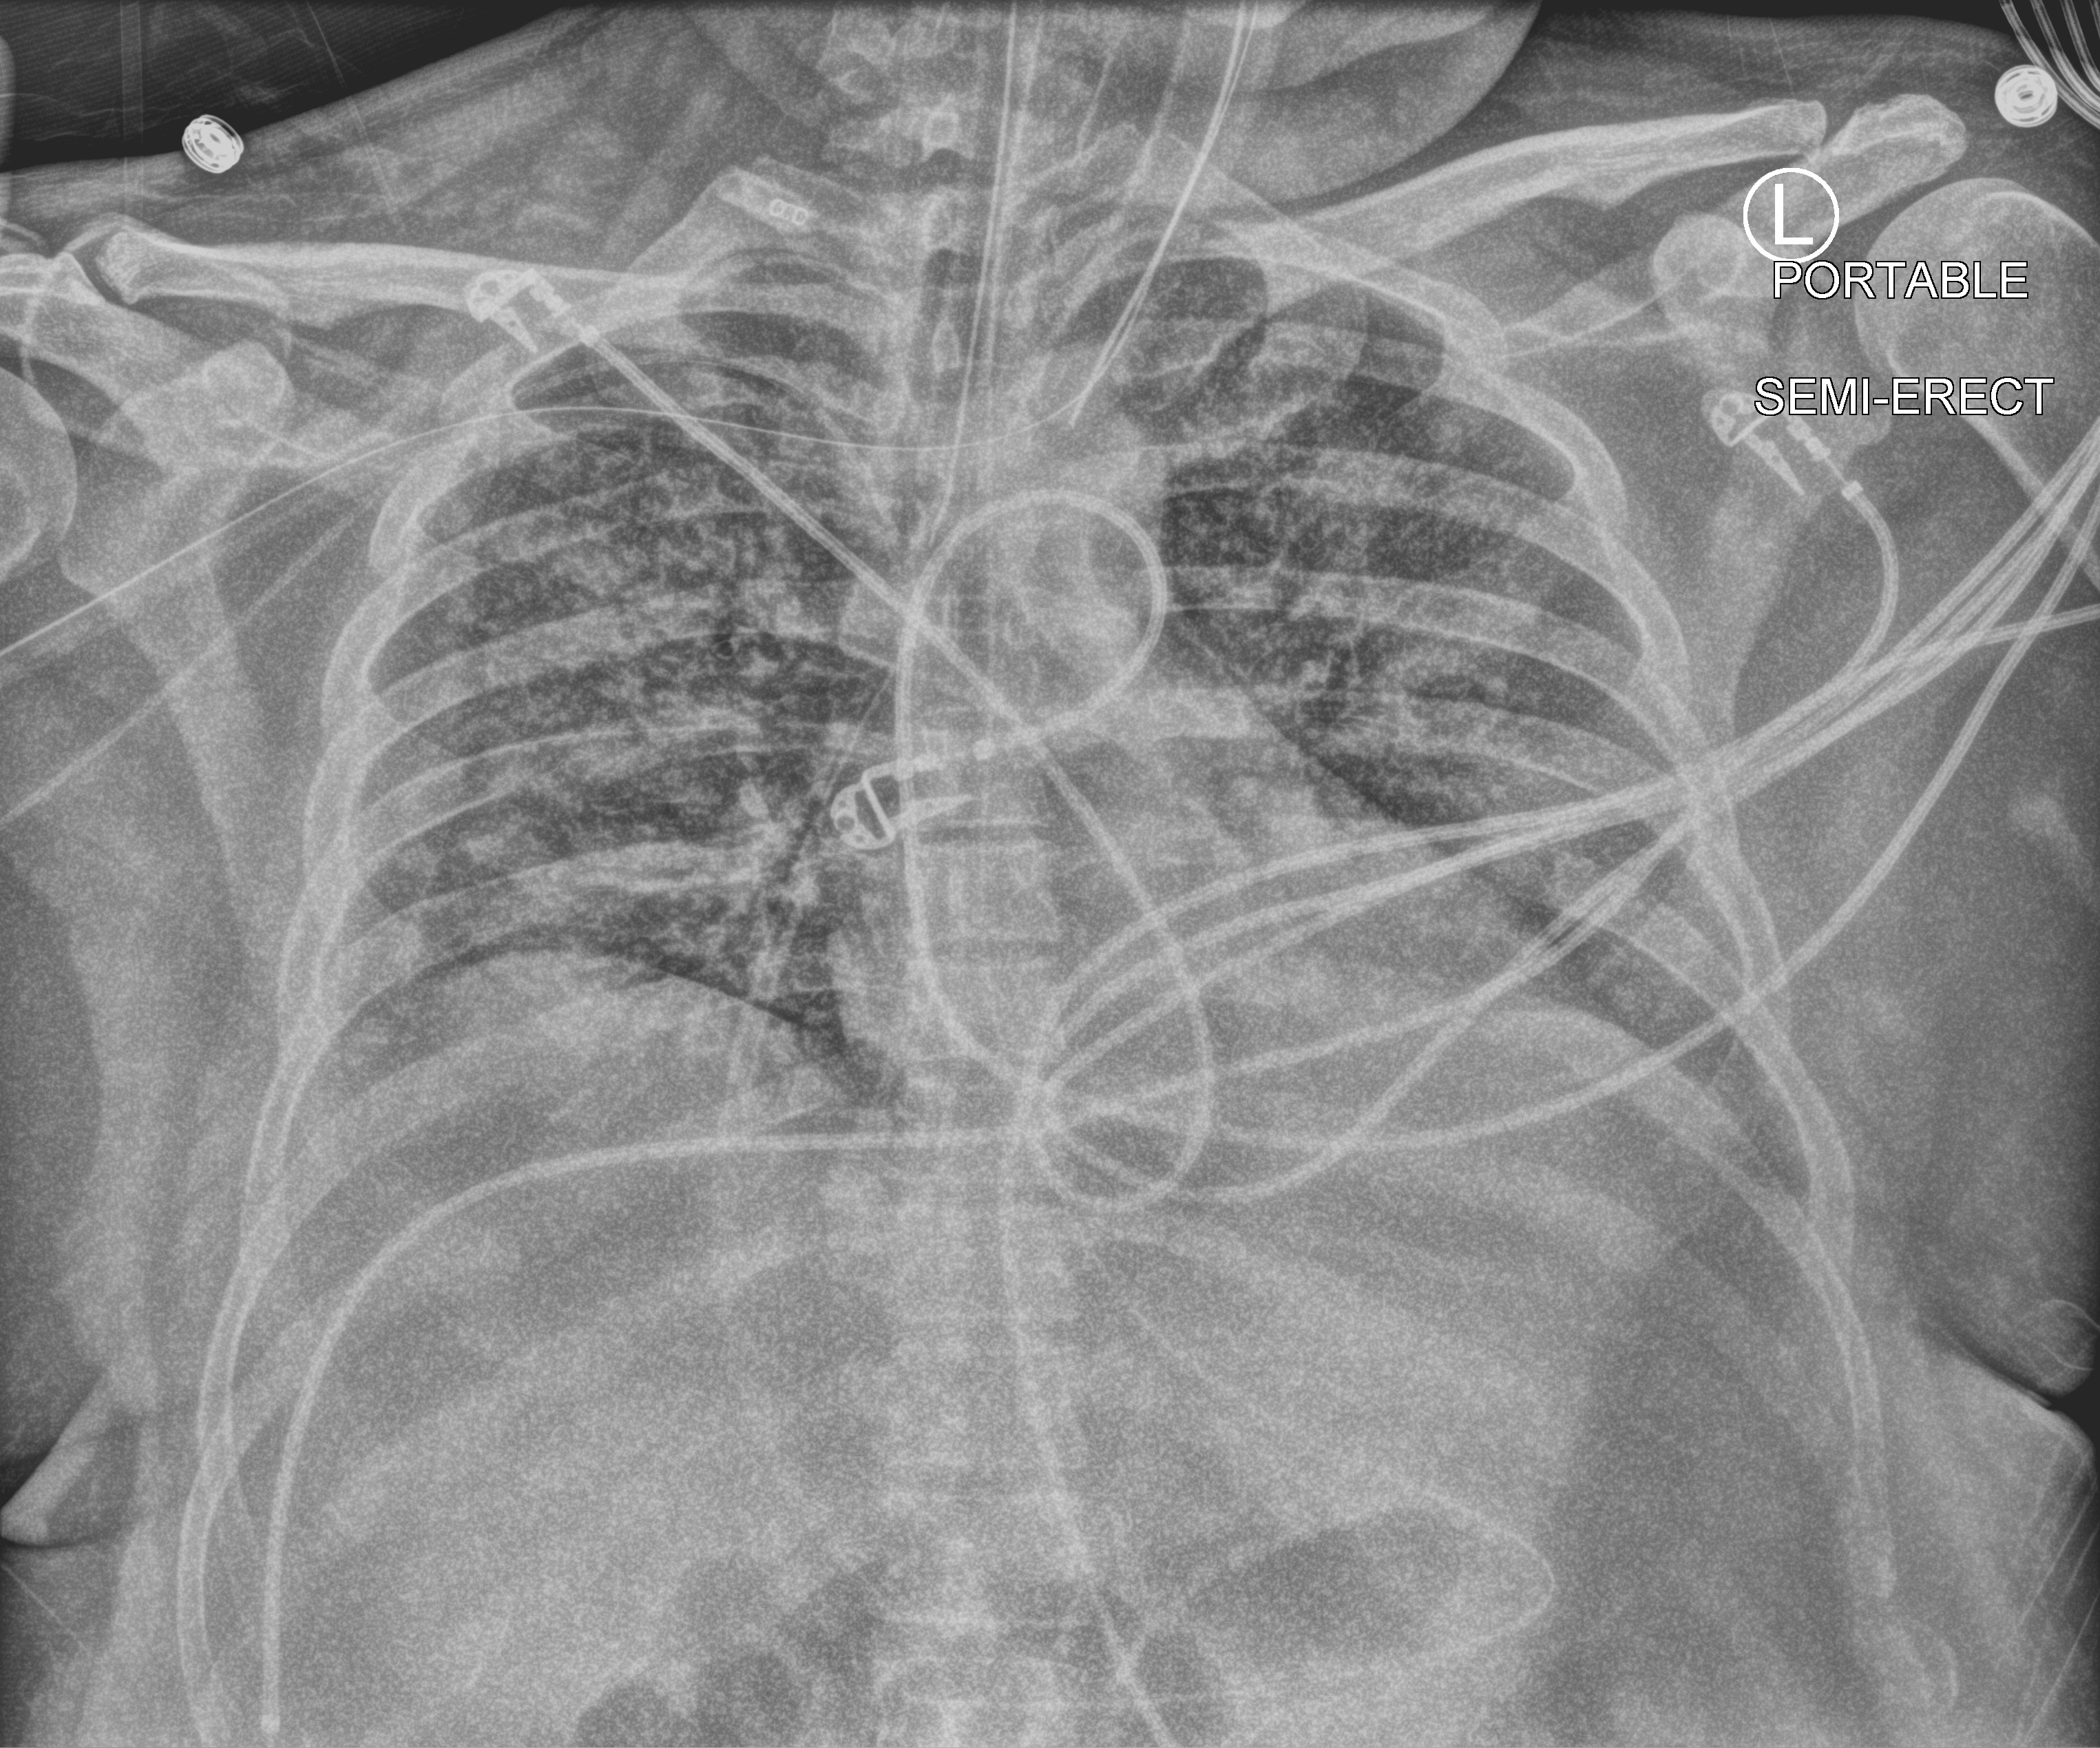
Bedside chest radiograph (computed radiography), anteroposterior (AP) projection. Male patient hospitalised with COVID-19, age 18–59 years.
From the hospital-stay record, not from the radiograph (when in the stay this image was taken is not recorded): diabetes (admission record): no.